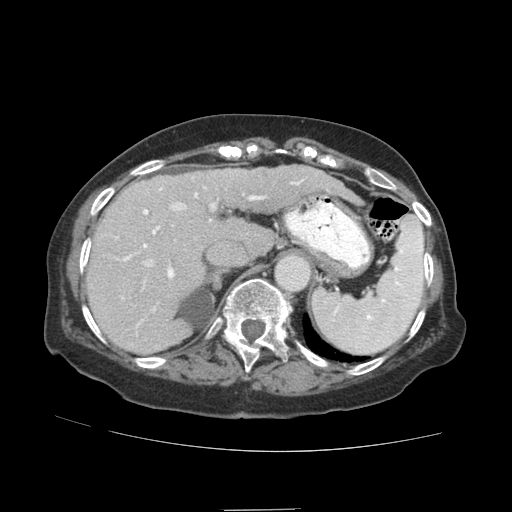
Contrast-enhanced abdominal CT (liver protocol), one axial slice; position 63 of 89 along the scan axis; soft-tissue window (W 400 / L 40 HU); 2.5 mm slice thickness; 512 × 512 image matrix. From the clinical record (not read from this slice): diagnosis: hepatocellular carcinoma (patient treated with transarterial chemoembolisation; whether this scan precedes or follows treatment is not stated here); TNM stage (as recorded): Stage-II; Child-Pugh class: A.
Outlined on this slice (semi-automatically segmented with operator editing):
- liver parenchyma outside the tumour (the mass and vessels are separate outlines, so this box may not span the whole liver): bounding box <86,166,332,352> (left, top, right, bottom; pixels)
- liver vessels: <114,176,304,335>